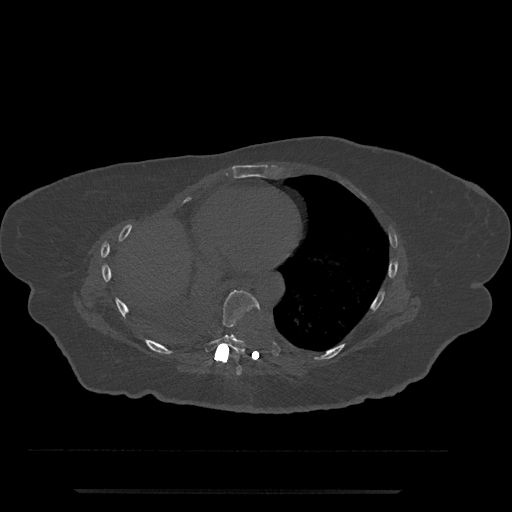
CT including the spine, one axial slice. 120 kVp. Bone window (W 1800 / L 400 HU). 0.5 mm slice thickness. 512 × 512 image matrix, field of view 440 × 440 mm. Female patient, age 51 years. From the clinical record (not read from this slice): primary cancer: neuro; vertebrae with lytic lesions (as recorded): T8.
Structures marked on this image (semi-automatically segmented with operator editing):
- T7 vertebra: bounding box <235,365,242,375> (left, top, right, bottom; pixels)
- T8 vertebra: <204,290,260,353>